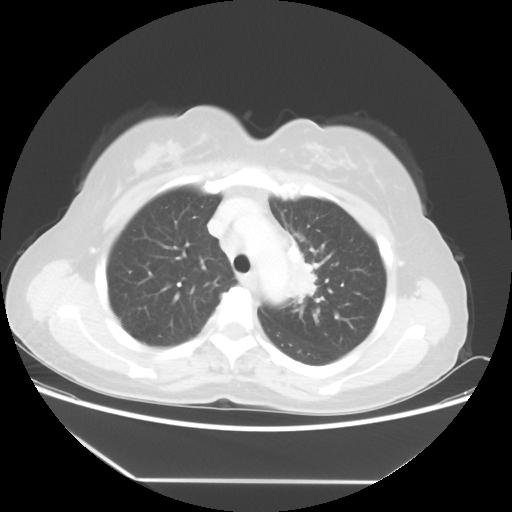
Chest CT, one axial slice. Position 39 of 52 along the scan axis. Reconstruction kernel STANDARD. Lung window (W 1500 / L -600 HU). 512 × 512 image matrix. Patient: female, 50 years. Case-level facts recorded for this patient, not image findings: clinical TNM (as recorded): T2 N3 M0.
Outlined on this slice (rectangle marked by the reading radiologist):
- lung tumour (recorded histology: adenocarcinoma): bounding box [x1, y1, x2, y2] px = [279, 244, 334, 314]